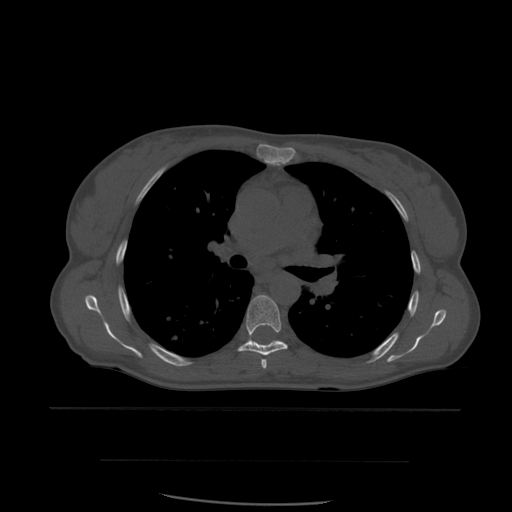
CT including the spine, one axial slice. Bone window (W 1800 / L 400 HU). 1.25 mm slice thickness. 512 × 512 image matrix, field of view 392 × 392 mm. Patient age 48 years. From the clinical record (not read from this slice): primary cancer: lung; vertebrae with lytic lesions (as recorded): T11.
Structures marked on this image (semi-automatic segmentation, software-assisted and operator-edited):
- T5 vertebra: bounding box (x1, y1, x2, y2) in pixels: (261, 359, 267, 369)
- T6 vertebra: (238, 295, 288, 356)